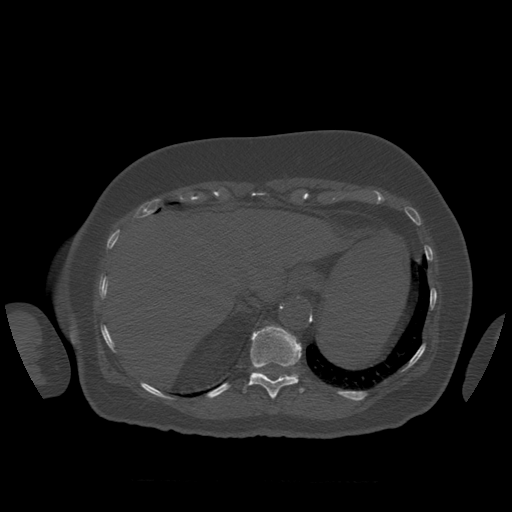
CT including the spine, one axial slice; slice 320 of 399 in the series (ordered by position); 120 kVp; bone window (W 1800 / L 400 HU); 1.25 mm slice thickness; 512 × 512 image matrix, field of view 404 × 404 mm. Patient age 81 years. Case-level facts recorded for this patient, not image findings: primary cancer: renal.
Structures marked on this image (semi-automatic segmentation, software-assisted and operator-edited):
- T11 vertebra: bounding box (x1, y1, x2, y2) in pixels: (244, 326, 305, 399)
- T12 vertebra: (291, 374, 298, 376)